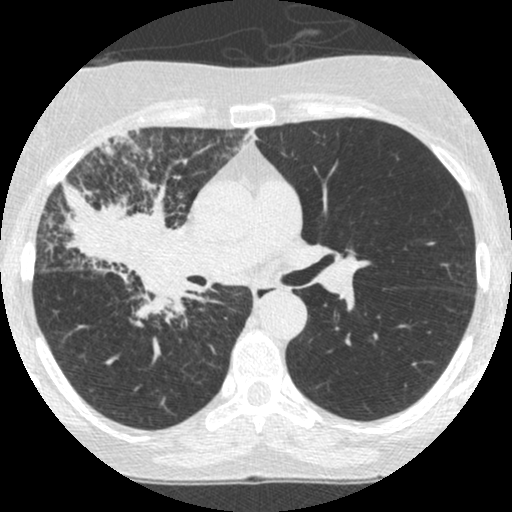
Low-dose screening chest CT, one axial slice. Position 150 of 253 along the scan axis. Reconstruction kernel STANDARD. Lung window (W 1500 / L -600 HU). 1.25 mm slice thickness. 512 × 512 image matrix, field of view 294 × 294 mm.
Outlined on this slice (manually delineated by an expert):
- lesion 2 (tumor, hilum of right lung): bounding box <62,179,186,322> (left, top, right, bottom; pixels)